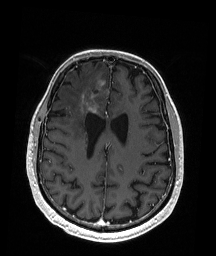
Brain MRI from a brain-tumour surgery series, one axial slice; position 70 of 192 along the scan axis; T1-weighted post-contrast; 1 mm slice thickness; 216 × 256 image matrix. Case-level facts recorded for this patient, not image findings: histopathology: Astrocytoma; WHO grade: 3; IDH mutation: yes.
Outlined on this slice (outlined manually by an expert reader):
- tumour: bounding box [x1, y1, x2, y2] px = [82, 95, 98, 115]